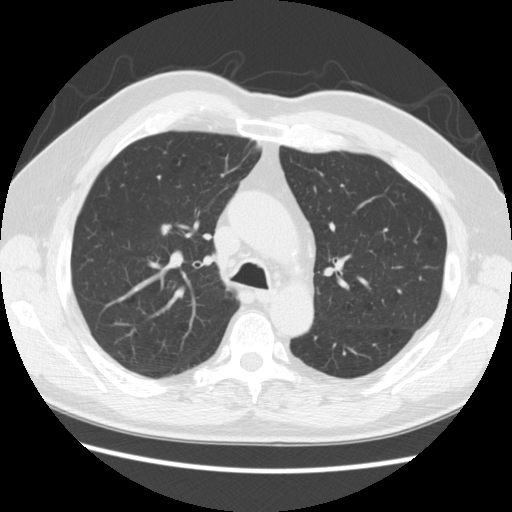
Low-dose screening chest CT, axial slice, baseline screening round, lung window (W 1500 / L -600 HU), 2.5 mm slice thickness, slice 85 of 259 in the series, 512 × 512 image matrix, field of view 360 × 360 mm. Male participant, aged 69 years at enrolment. Former smoker at enrolment.
Lesion marked by an expert reader, bounding box [x1, y1, x2, y2] px = [149, 217, 192, 249]. The exam's reader record, not a measurement of the box and not confirmed to be the same lesion: non-calcified nodule or mass ≥4 mm, right upper lobe, 9 × 7 mm, poorly defined margins, soft tissue attenuation. Official screen result: positive, change unspecified: nodule(s) >= 4 mm or enlarging nodule(s), mass(es), or other non-specific abnormalities suspicious for lung cancer. Later outcome: lung cancer diagnosed 50 days after this screen — adenocarcinoma, NOS, right upper lobe, moderately differentiated (G2), stage IA (AJCC 6th edition), 9 mm at pathology.